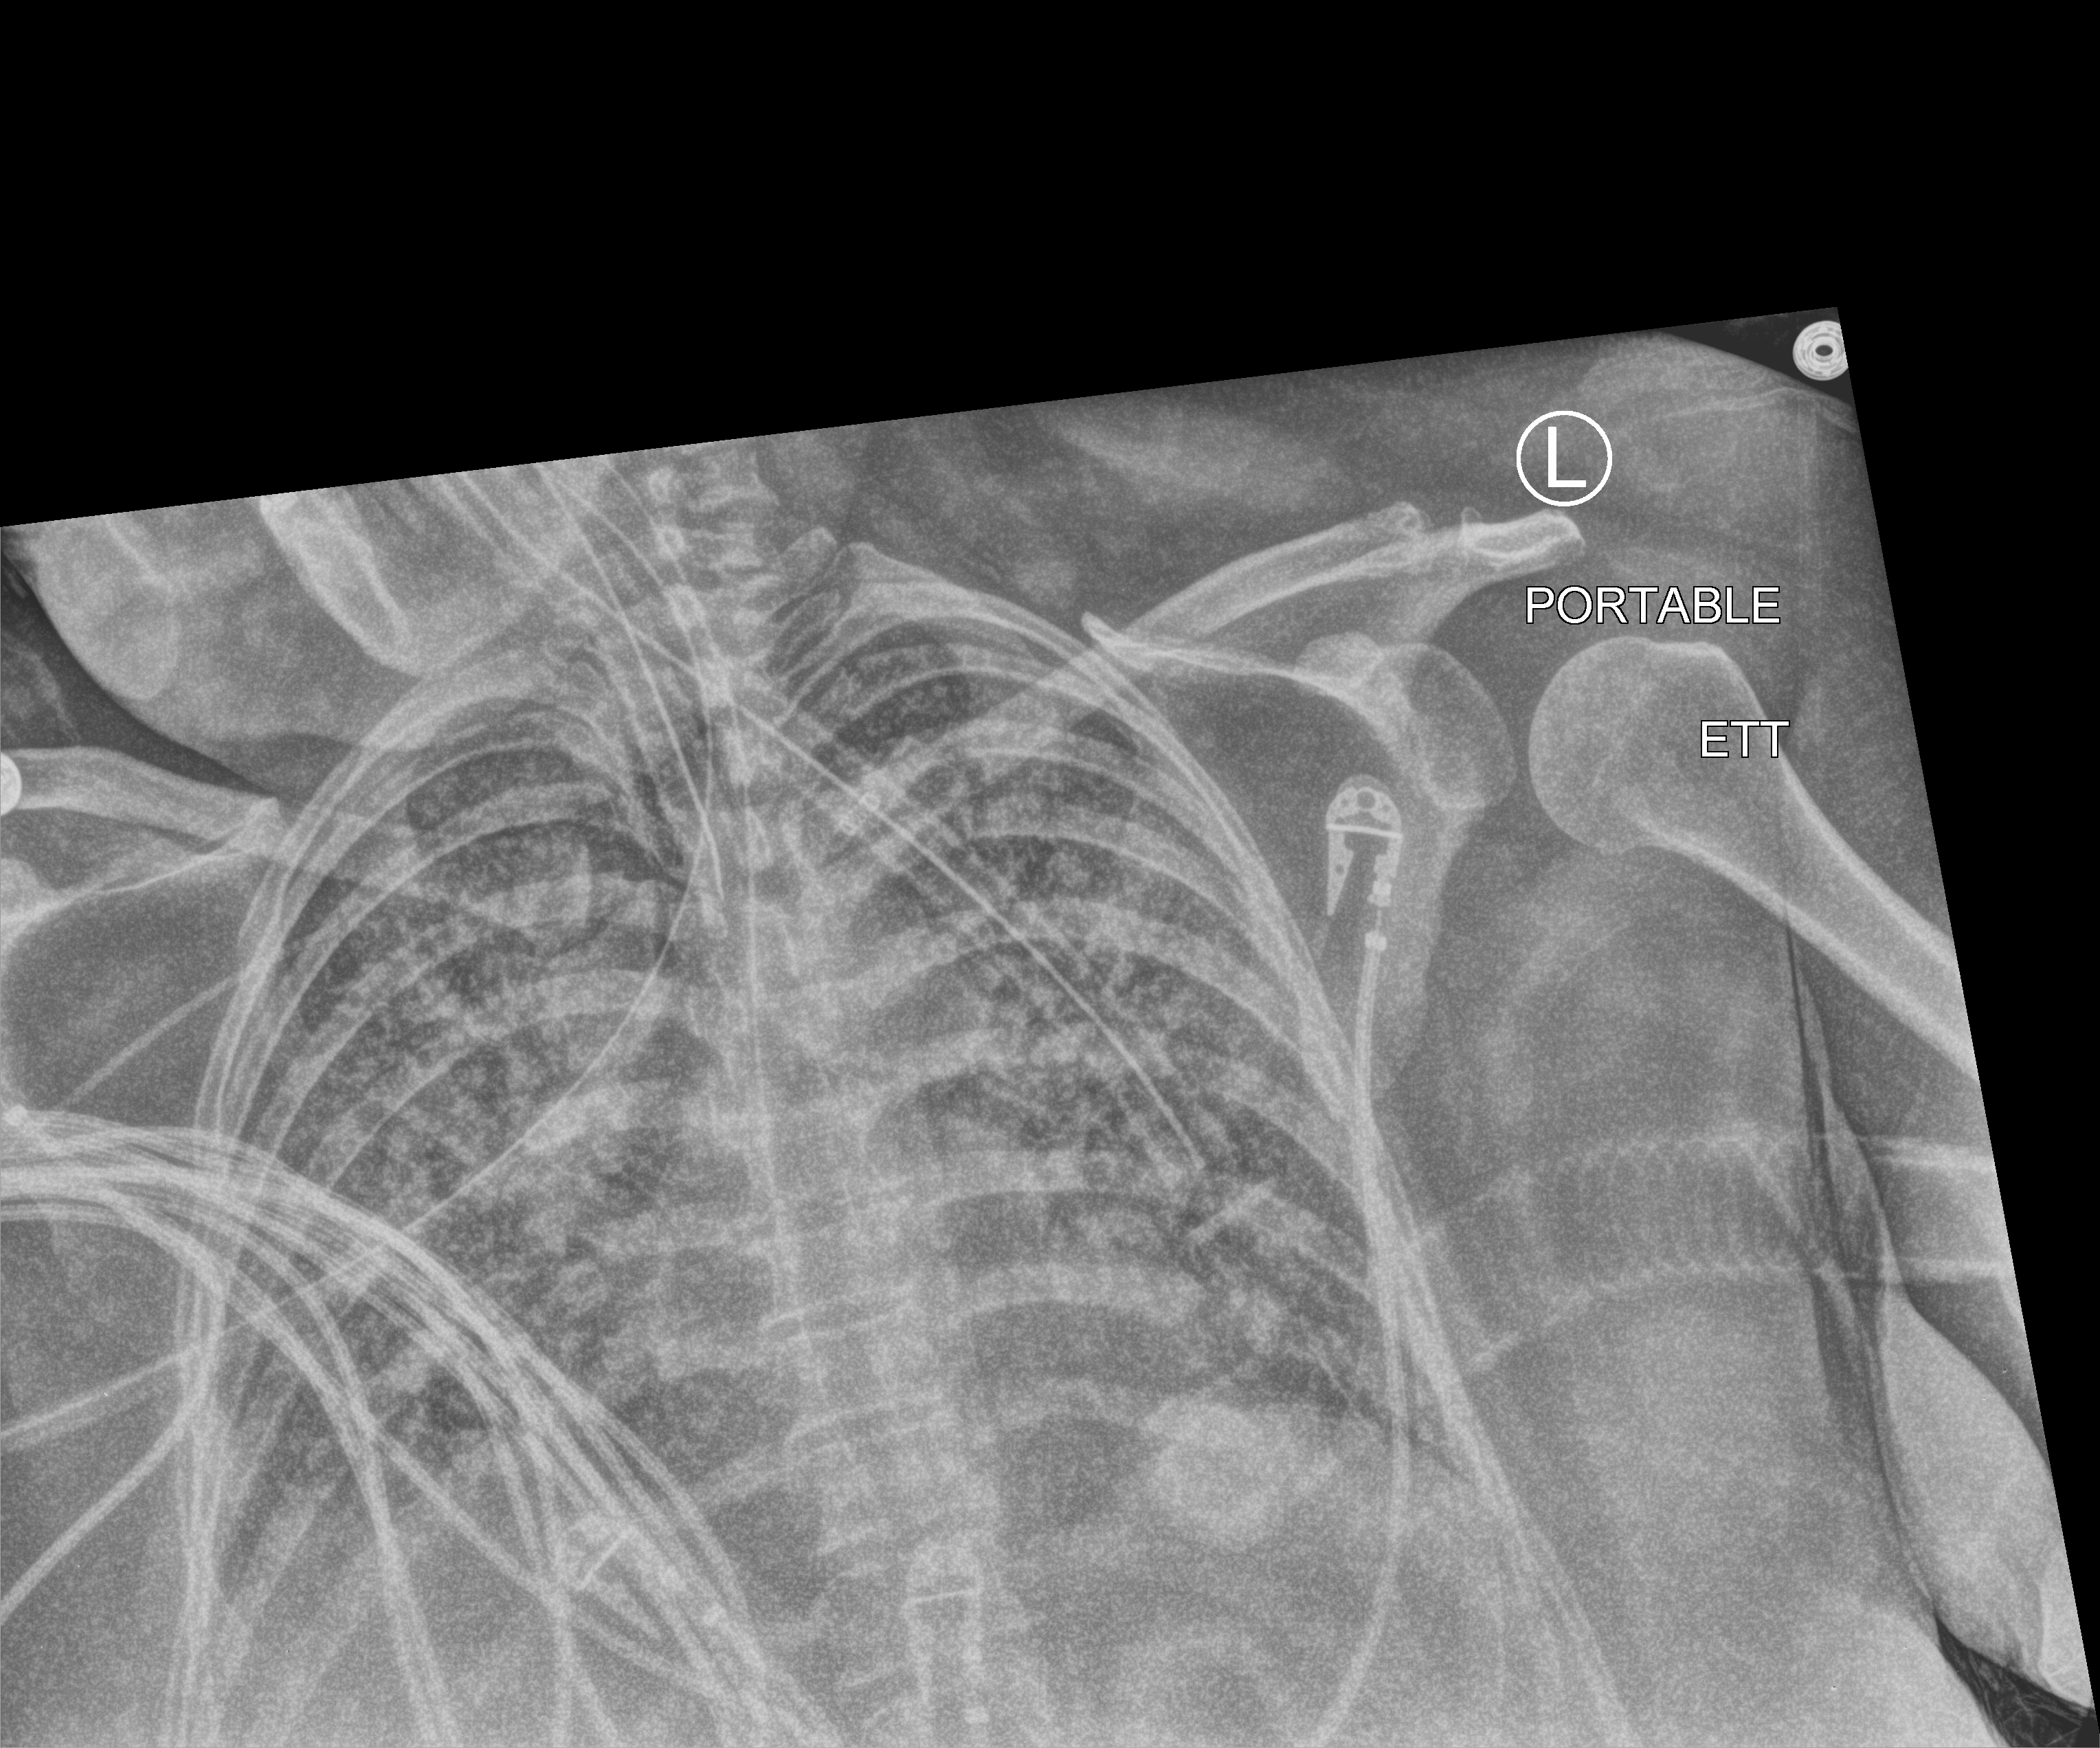
Bedside chest radiograph (computed radiography). Female patient hospitalised with COVID-19, age 18–59 years.
From the hospital-stay record, not from the radiograph (when in the stay this image was taken is not recorded):
- mechanically ventilated during this hospital stay: yes